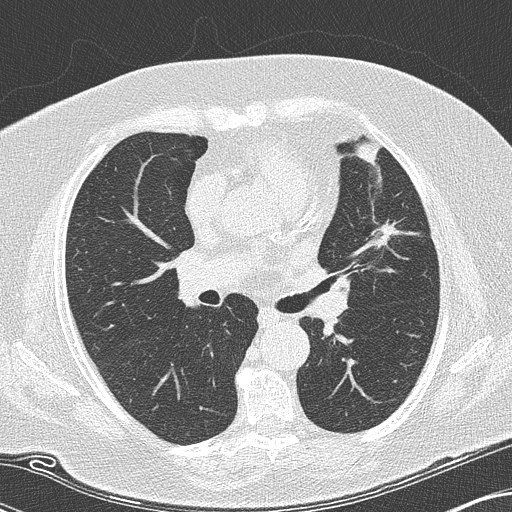
Low-dose screening chest CT, axial slice, second annual screen, lung window (W 1500 / L -600 HU), 2 mm slice thickness, 120 kVp, slice 59 of 151 in the series, 512 × 512 image matrix, field of view 330 × 330 mm. Female, age 73 years at enrolment. Current smoker at enrolment.
Lesion marked by an expert reader, bounding box <368,214,406,254> (left, top, right, bottom; pixels). The screening reader recorded 2 non-calcified nodules or masses ≥4 mm on this exam (lingula, right lower lobe); which of them this box marks is not recorded. Participant outcome: lung cancer diagnosed 123 days after this screen — adenocarcinoma, NOS, left upper lobe, moderately differentiated (G2), stage IIIB (AJCC 6th edition), 12 mm at pathology.